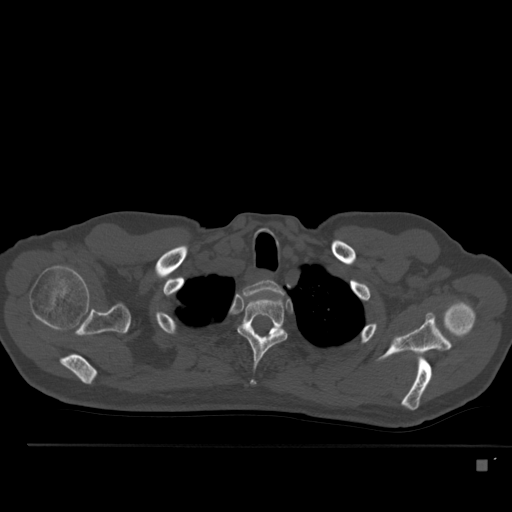
CT including the spine, one axial slice; slice 411 of 517 in the series (ordered by position); 120 kVp; bone window (W 1800 / L 400 HU); 1.5 mm slice thickness; 512 × 512 image matrix, field of view 408 × 408 mm. Patient: male, 70 years. From the clinical record (not read from this slice): primary cancer: renal; vertebrae with lytic lesions (as recorded): T4, T6, T10, T12, L3, L4, L5.
Outlined on this slice (semi-automatically segmented with operator editing):
- T1 vertebra: bounding box [x1, y1, x2, y2] px = [244, 280, 281, 295]
- T2 vertebra: [237, 296, 288, 385]
- T3 vertebra: [226, 323, 283, 352]